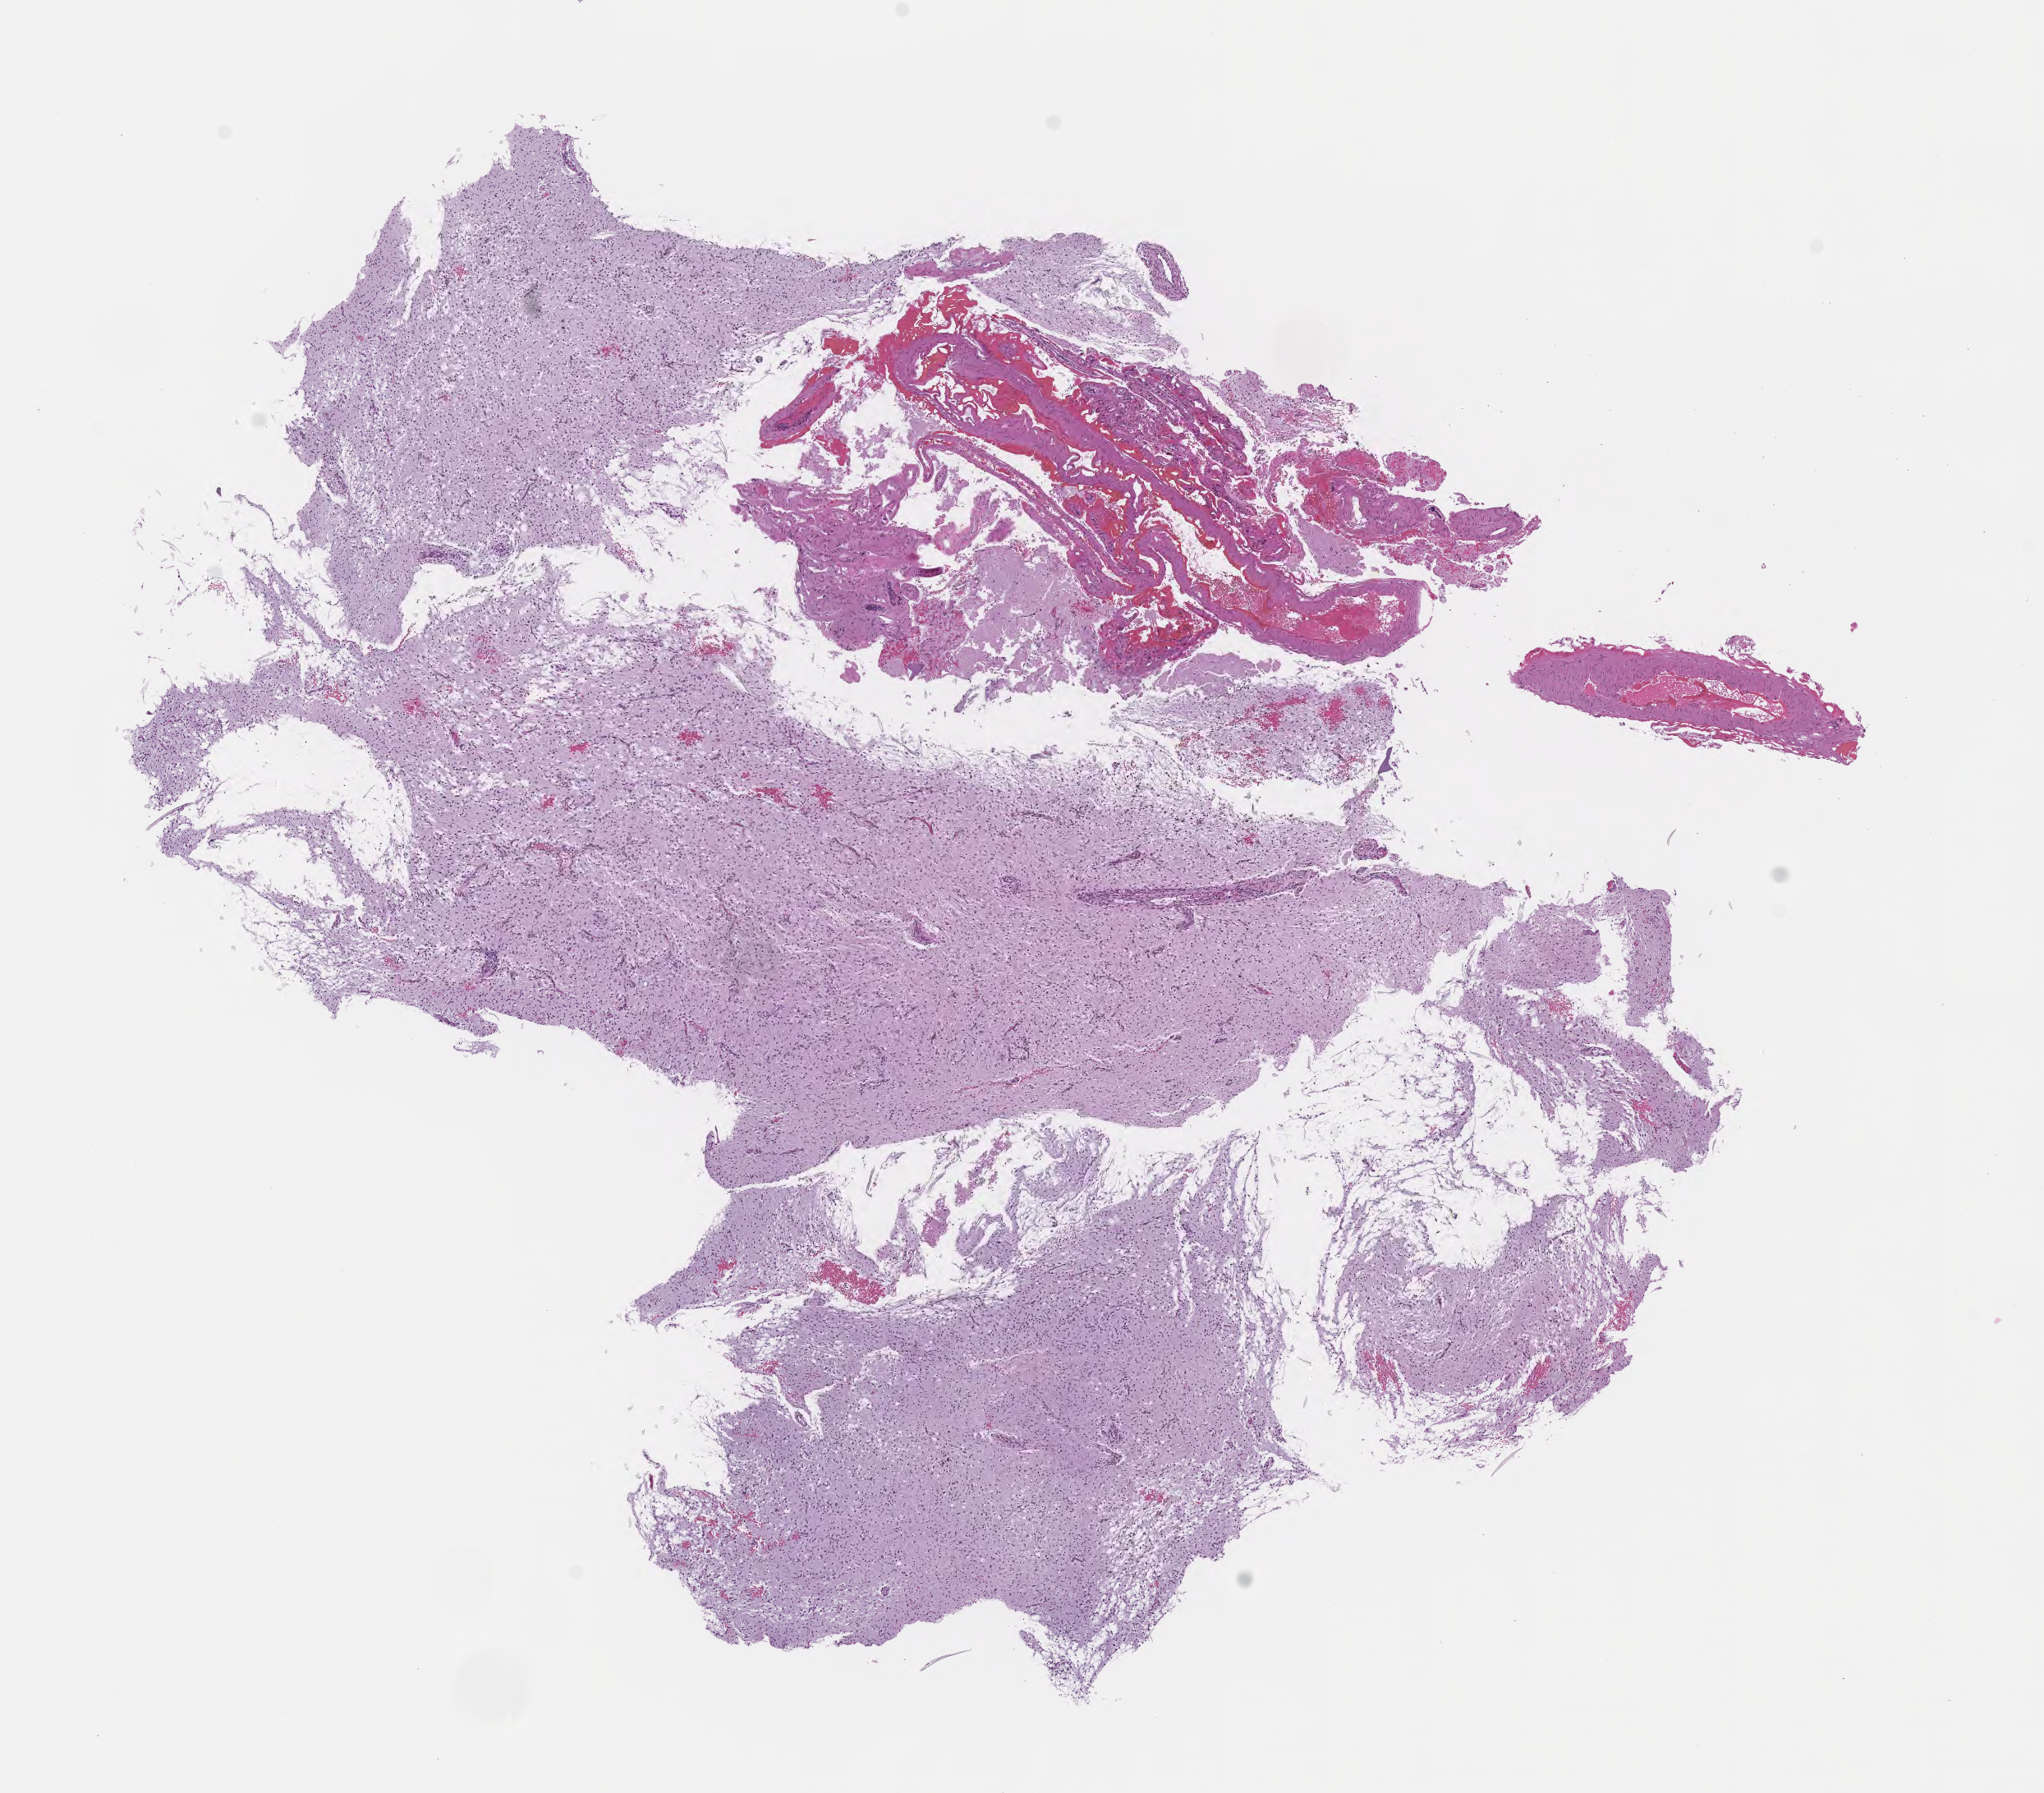
H&E whole-slide image of tumor tissue from the brain, whole scanned area (about 10.1 x 8.8 mm) shown as a low-resolution overview, formalin-fixed, paraffin-embedded (FFPE) tissue. Male patient, age 159 months.
Diagnosis (ICD-O-3 morphology term): Neoplasm, malignant.